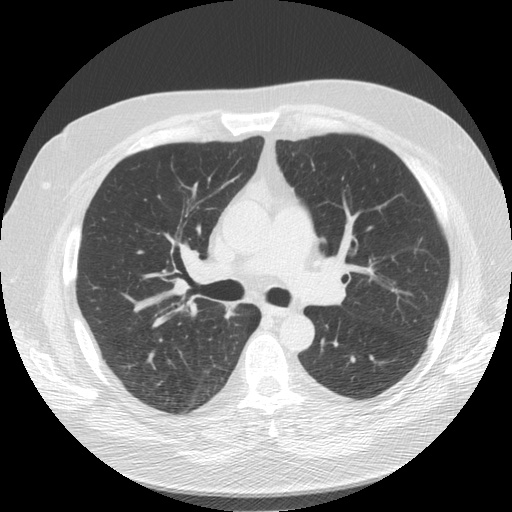
Low-dose screening chest CT, one axial slice; position 89 of 136 along the scan axis; reconstruction kernel STANDARD; lung window (W 1500 / L -600 HU); 2.5 mm slice thickness; 512 × 512 image matrix, field of view 360 × 360 mm.
Structures marked on this image (outlined manually by an expert reader):
- lesion 1 (tumor, upper lobe of right lung): bounding box [x1, y1, x2, y2] px = [224, 305, 237, 318]